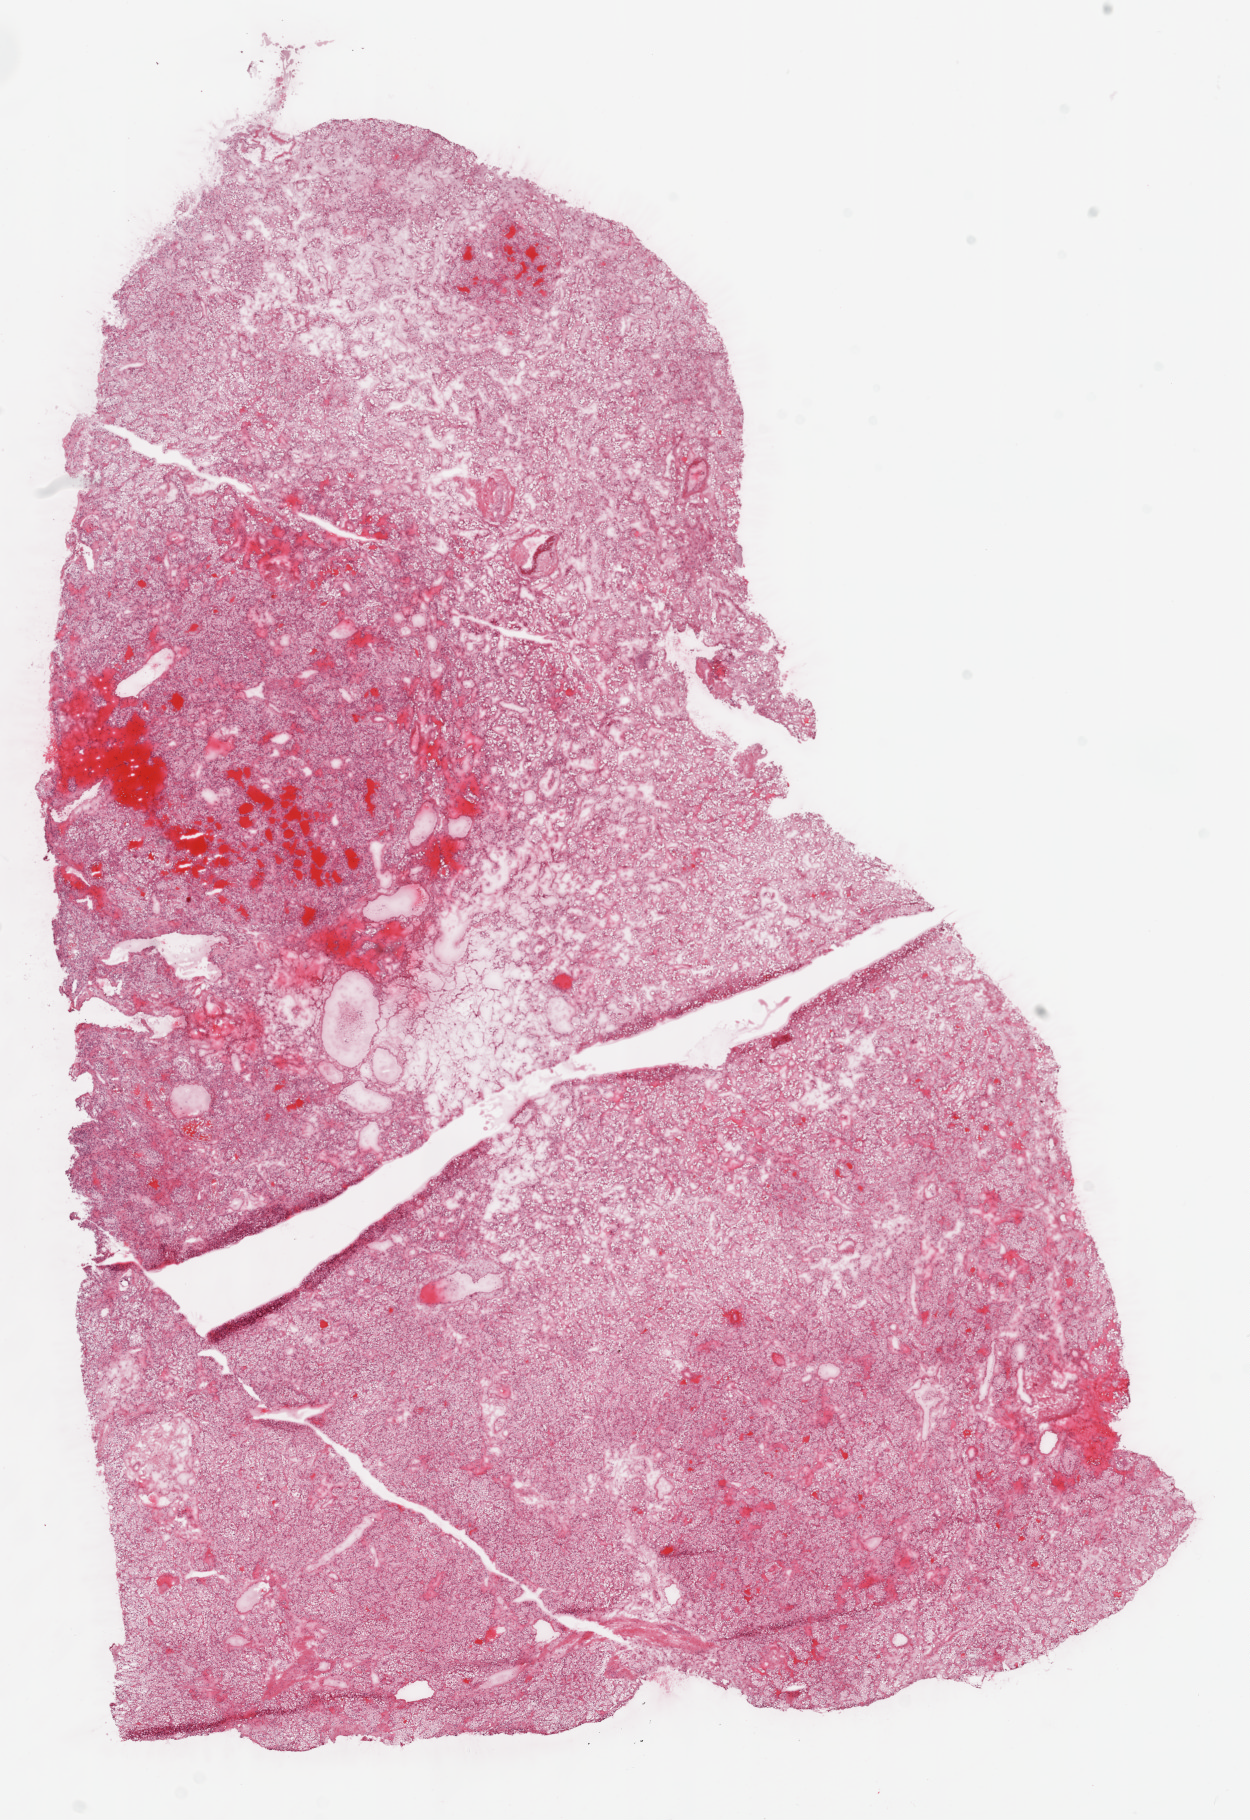
Whole-slide histology image, Hematoxylin and eosin (H&E) stained, shown as a low-resolution overview of the whole scanned area (about 10.0 x 14.6 mm, from a 20x scan). Frozen section from the top of the tissue portion. Sample: primary tumour, kidney. Male patient; age at initial diagnosis 54 years. Histologic grade: G2 (moderately differentiated). Pathologist review of this section (percent, as recorded): tumour cells 90%, tumour nuclei 85%, normal cells 0%, stromal cells 10%, necrosis 0%.
Histologic diagnosis: Clear cell adenocarcinoma, NOS. TNM: T1a NX M0. AJCC pathologic stage: I.